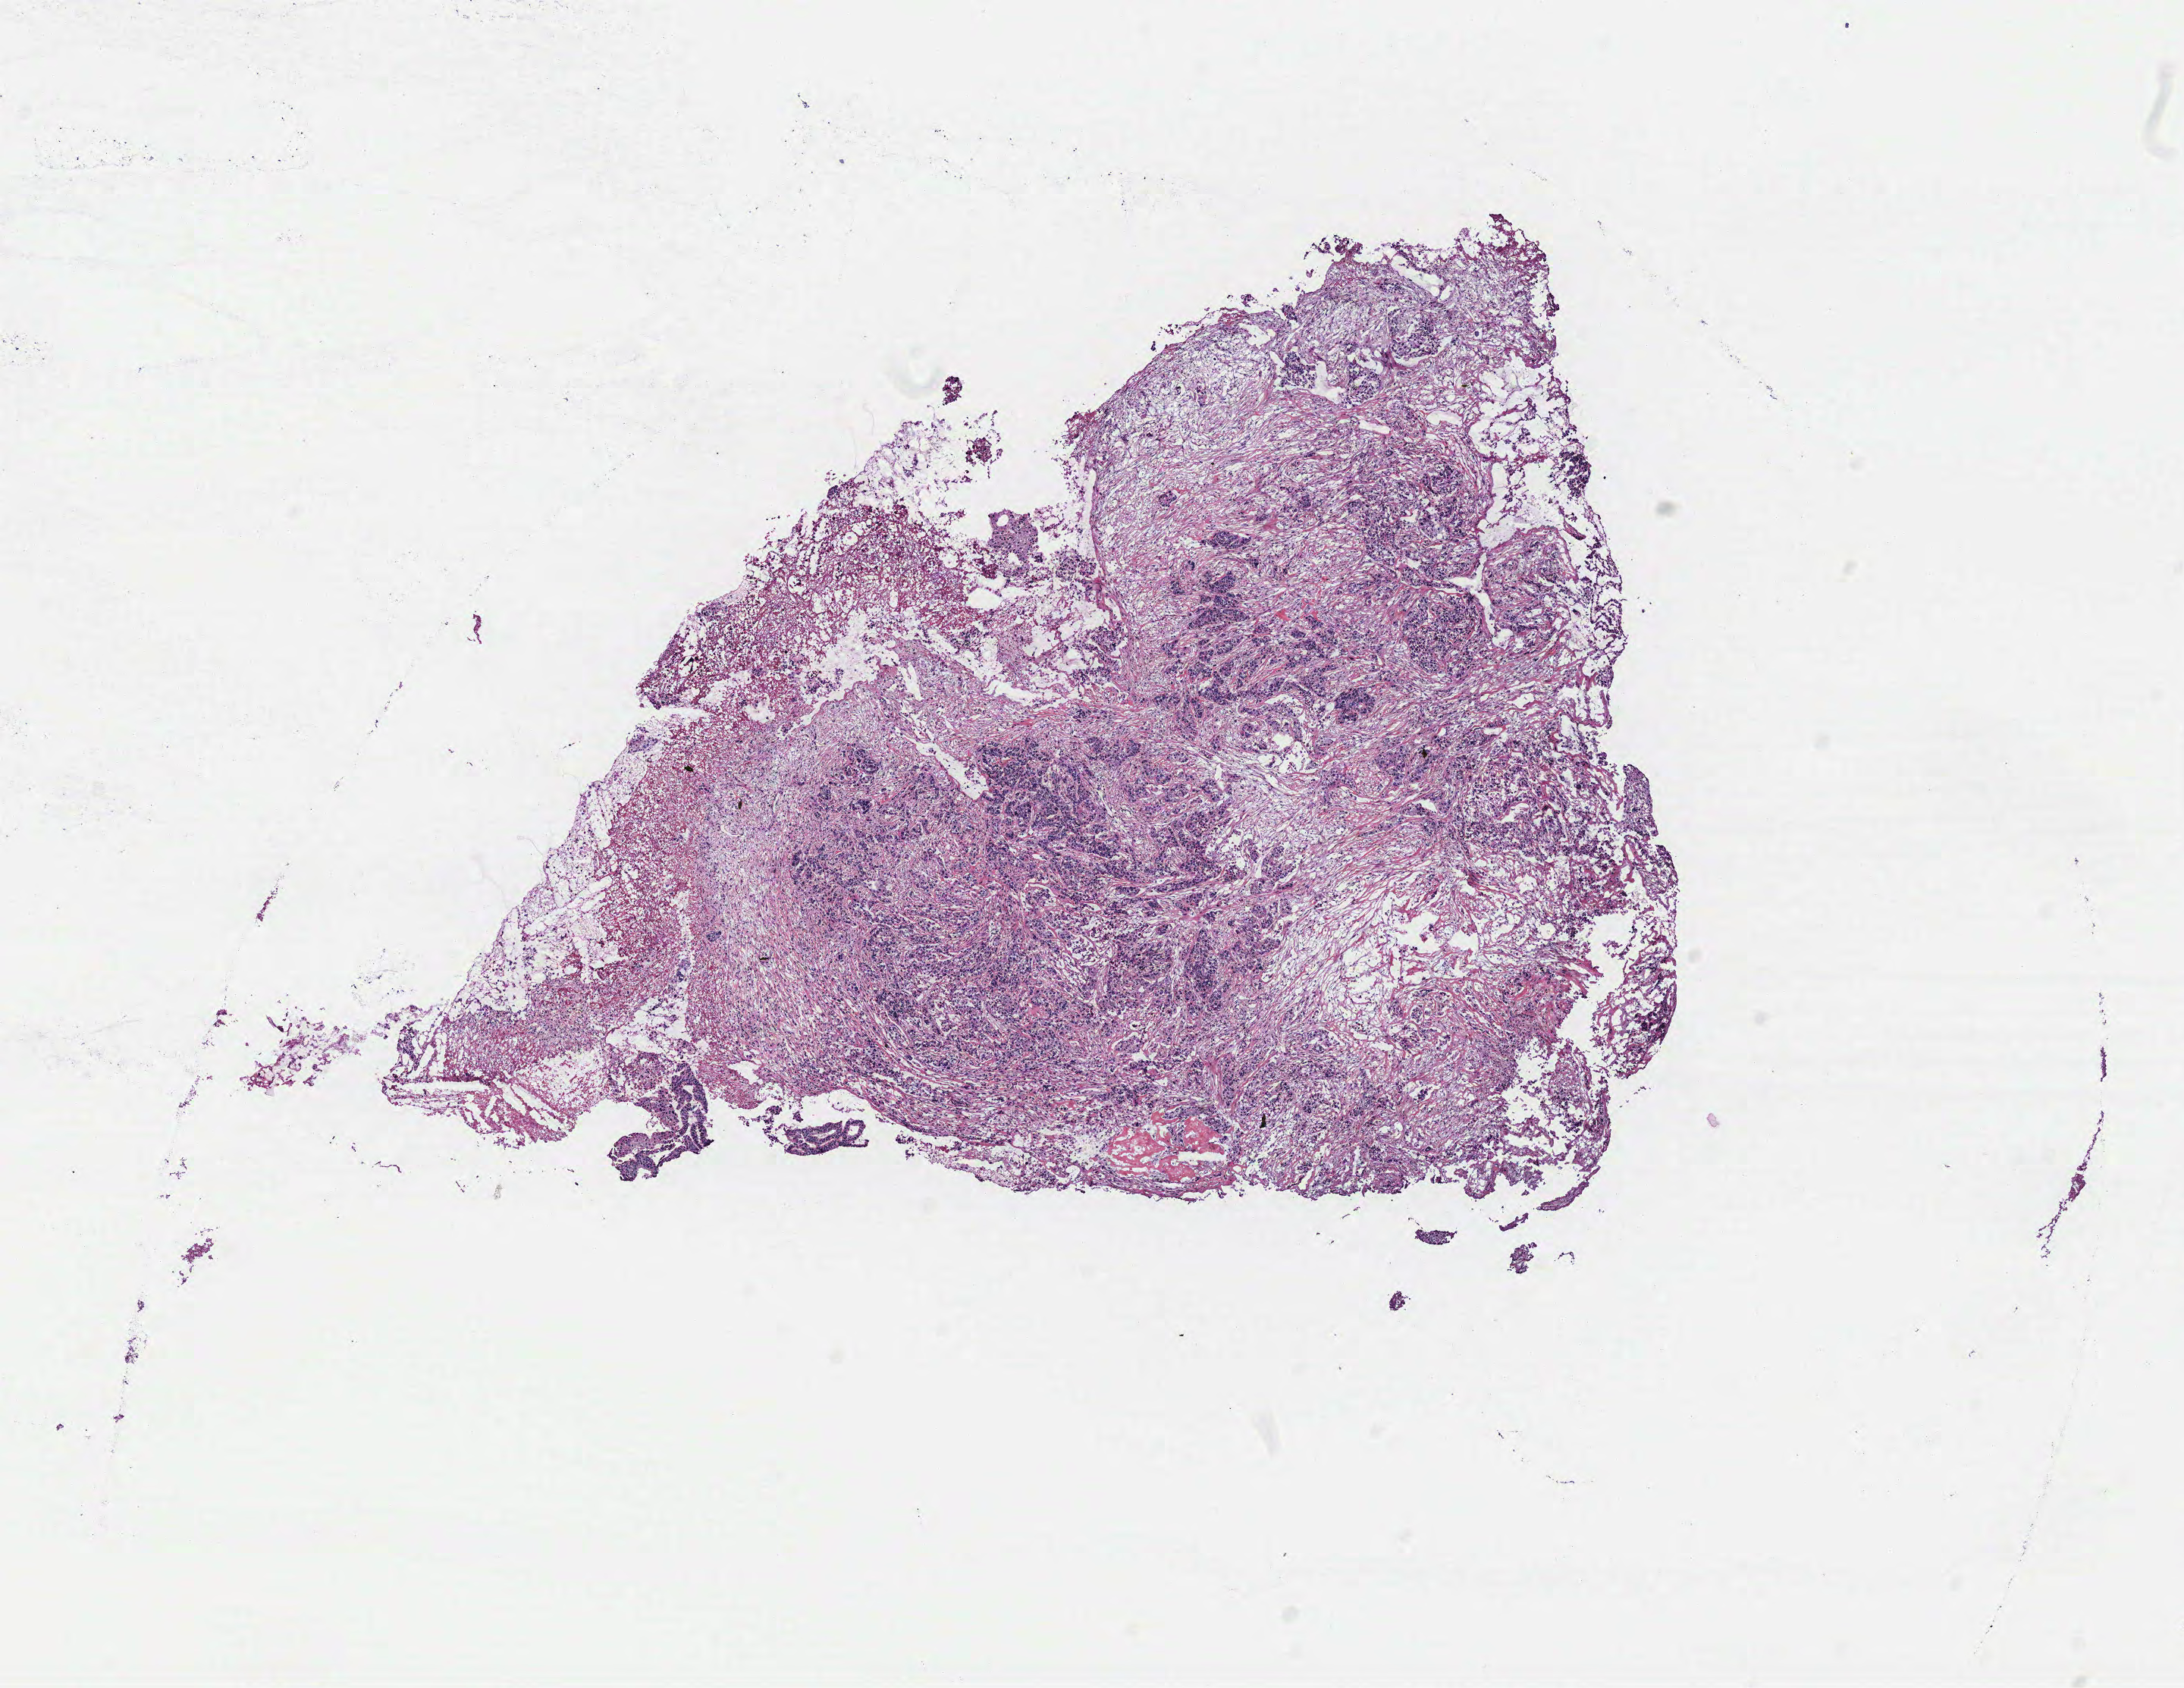
Hematoxylin and eosin (H&E) stained whole-slide image — low-resolution overview of the scanned area, about 11.5 x 8.9 mm (from a 40x scan); tumour tissue sample, ovary. 55-year-old female patient.
Patient diagnosis (cohort enrolment): ovarian cancer (ovary).